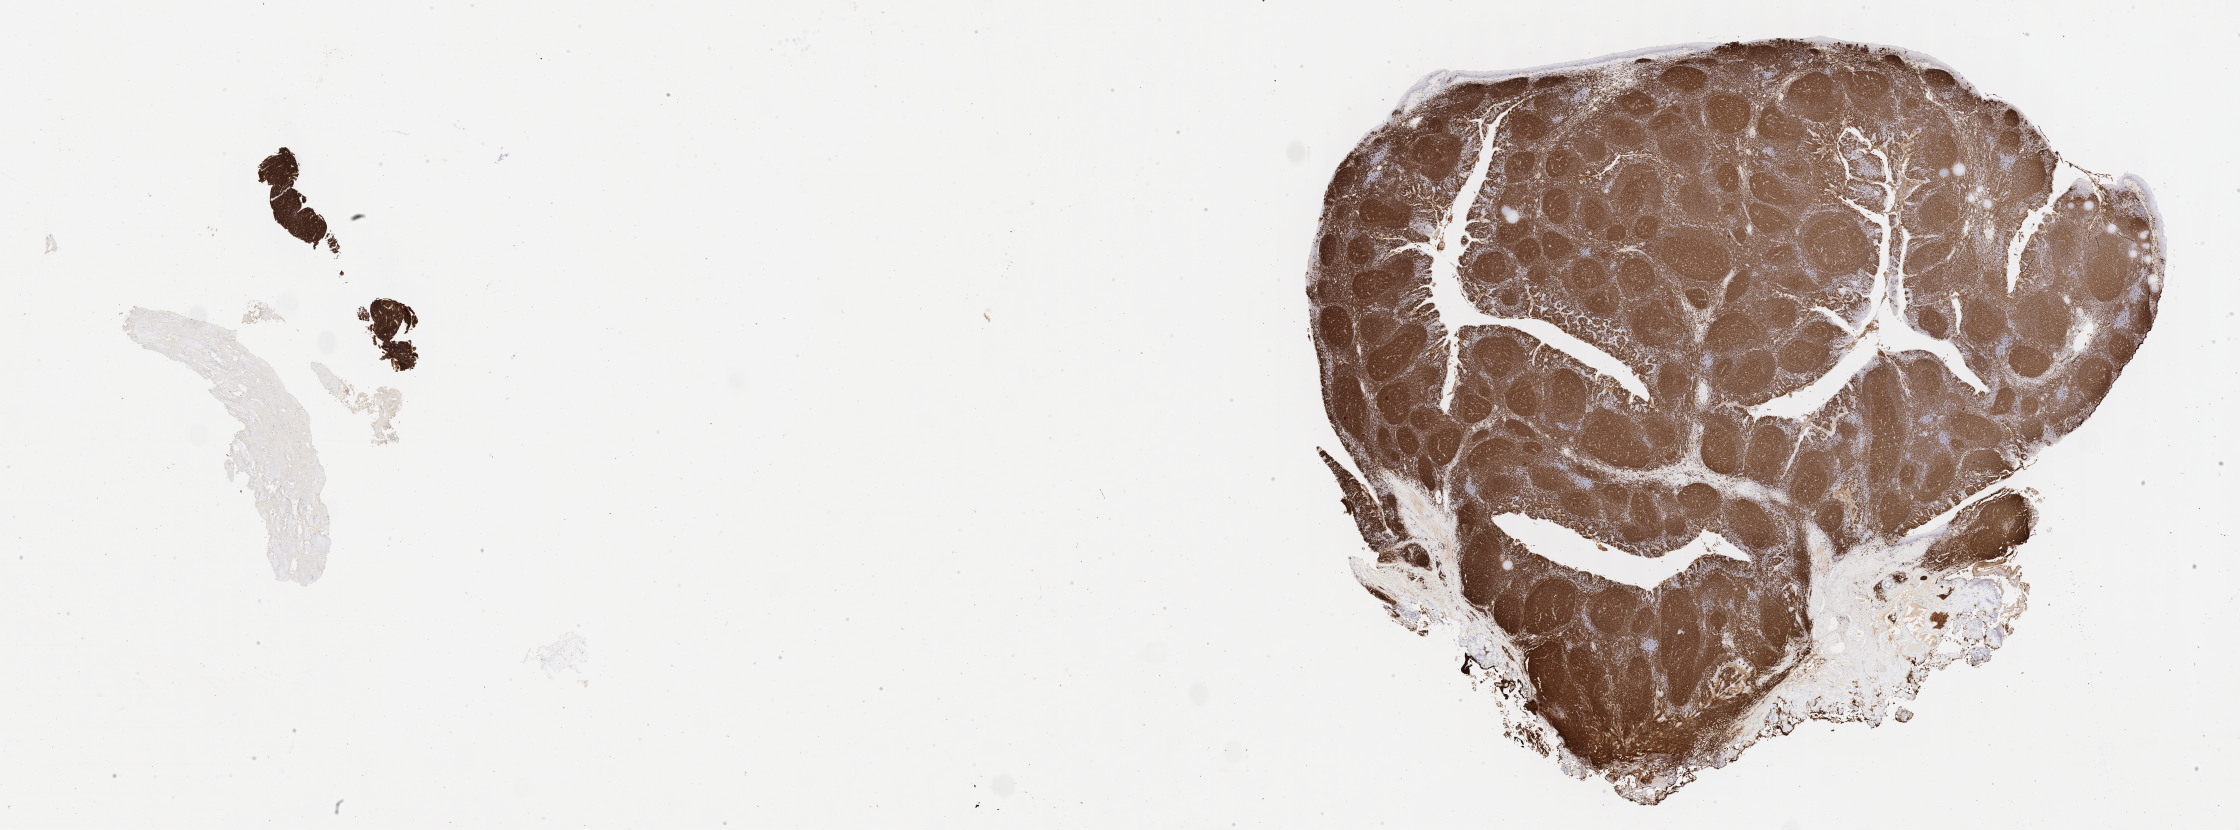
IHC for CD20, whole-slide image — low-resolution overview of the scanned area, about 36.2 x 13.4 mm. Tumor tissue. Site: liver. Male patient.
• diagnosis: Burkitt lymphoma, NOS